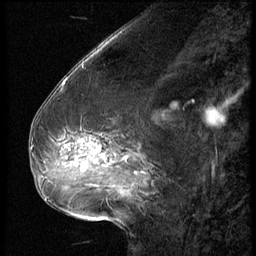
Breast MRI (dynamic contrast-enhanced), one sagittal slice. Position 23 of 62 along the scan axis. 3 images stored at this slice position (order not interpretable as contrast timing). 1.5 T. TE 4.2 ms, TR 9 ms. 256 × 256 image matrix. Patient: female, 54 years. Case-level facts recorded for this patient, not image findings: setting: breast cancer imaged before/during neoadjuvant chemotherapy; receptor status: HR-positive, HER2-negative.
Annotated regions visible in this slice (semi-automatically segmented with operator editing):
- analysis volume of interest (the breast-tissue region the enhancement analysis was run in; not a lesion): bounding box (x1, y1, x2, y2) in pixels: (42, 126, 146, 183)
- tumour enhancement mask (voxels above the 140 % enhancement threshold inside the analysis volume of interest): (81, 147, 101, 170)